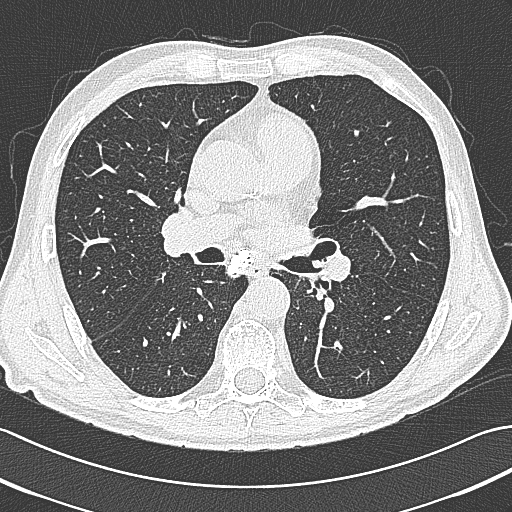
Chest CT (low-dose screening protocol), one axial image. First (baseline) screen. Lung window (W 1500 / L -600 HU). Lung (sharp) reconstruction kernel (B80f). Male, age 65 years at enrolment. Current smoker at enrolment.
Expert-annotated lung lesion, box from (x=303, y=229) to (x=345, y=280) px. No non-calcified nodule or mass ≥4 mm was recorded by the screening reader at this exam. Lung cancer was diagnosed 161 days after this screen: large cell neuroendocrine carcinoma, left hilum, left main stem bronchus, stage IIIB (AJCC 6th edition), 70 mm at pathology.